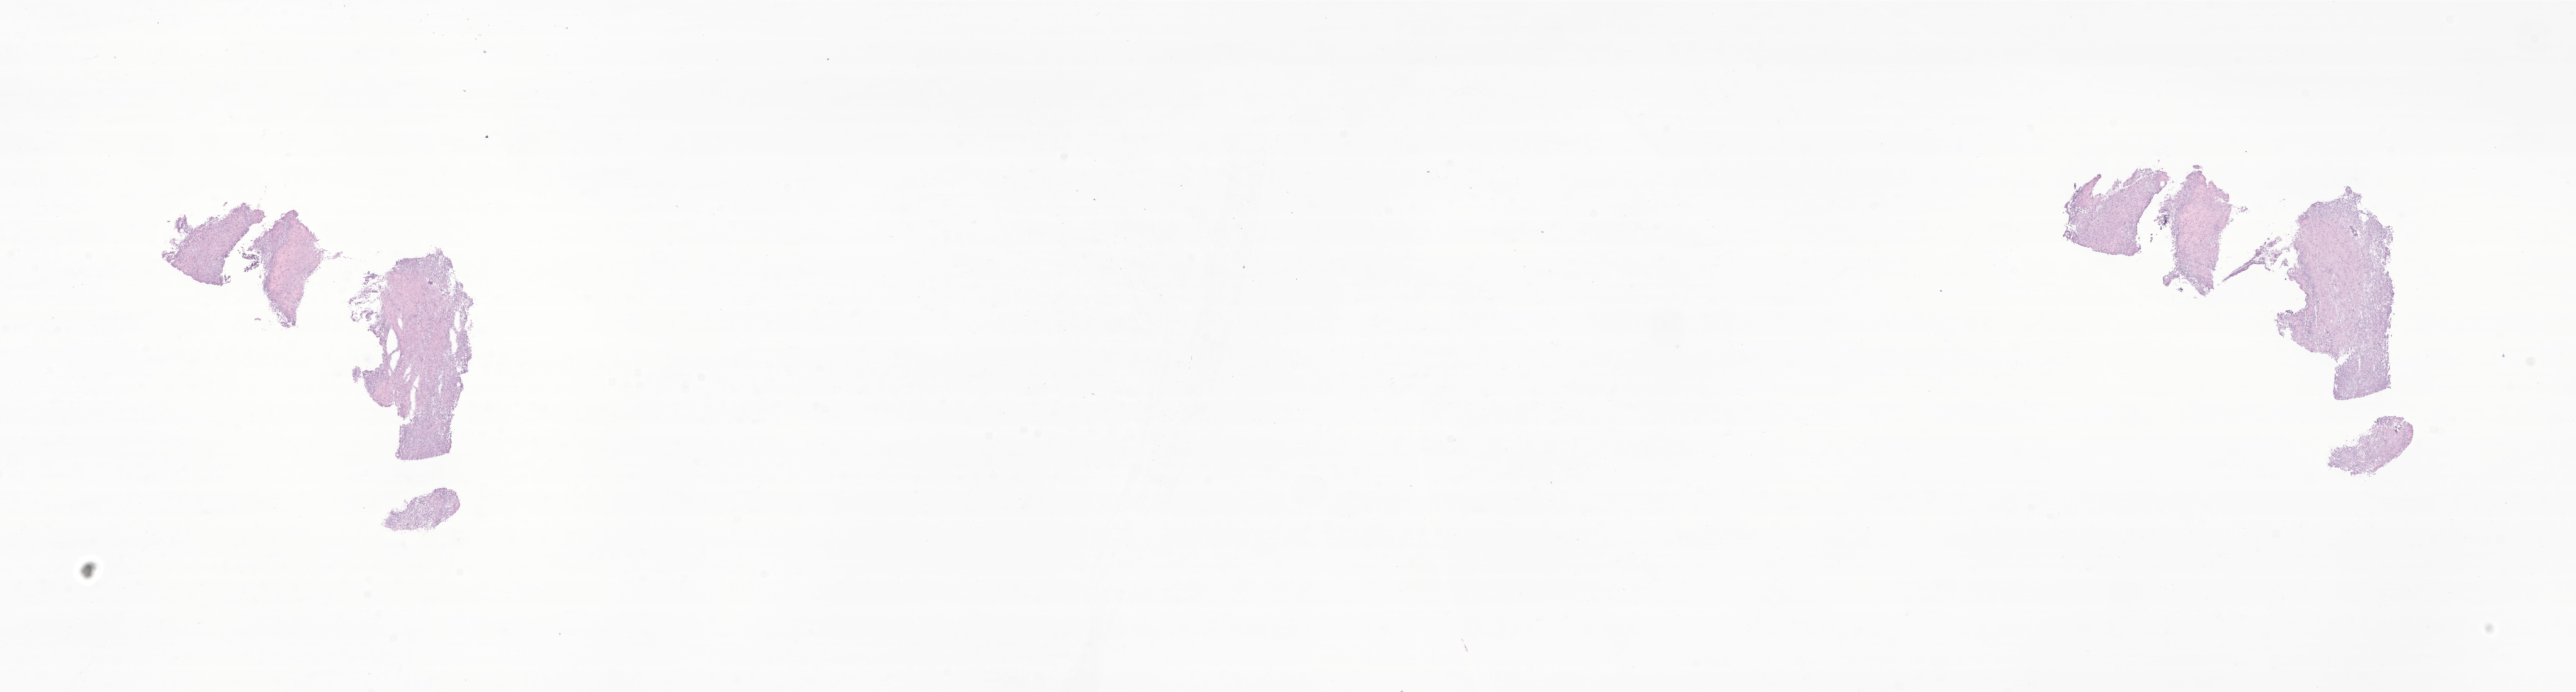
H&E whole-slide image of tumor tissue from the brain — whole scanned area (about 30.6 x 8.2 mm) shown as a low-resolution overview, frozen section (OCT-embedded). Patient: female, age 143 months (11 years 11 months).
Recorded diagnosis: Glioma, malignant.